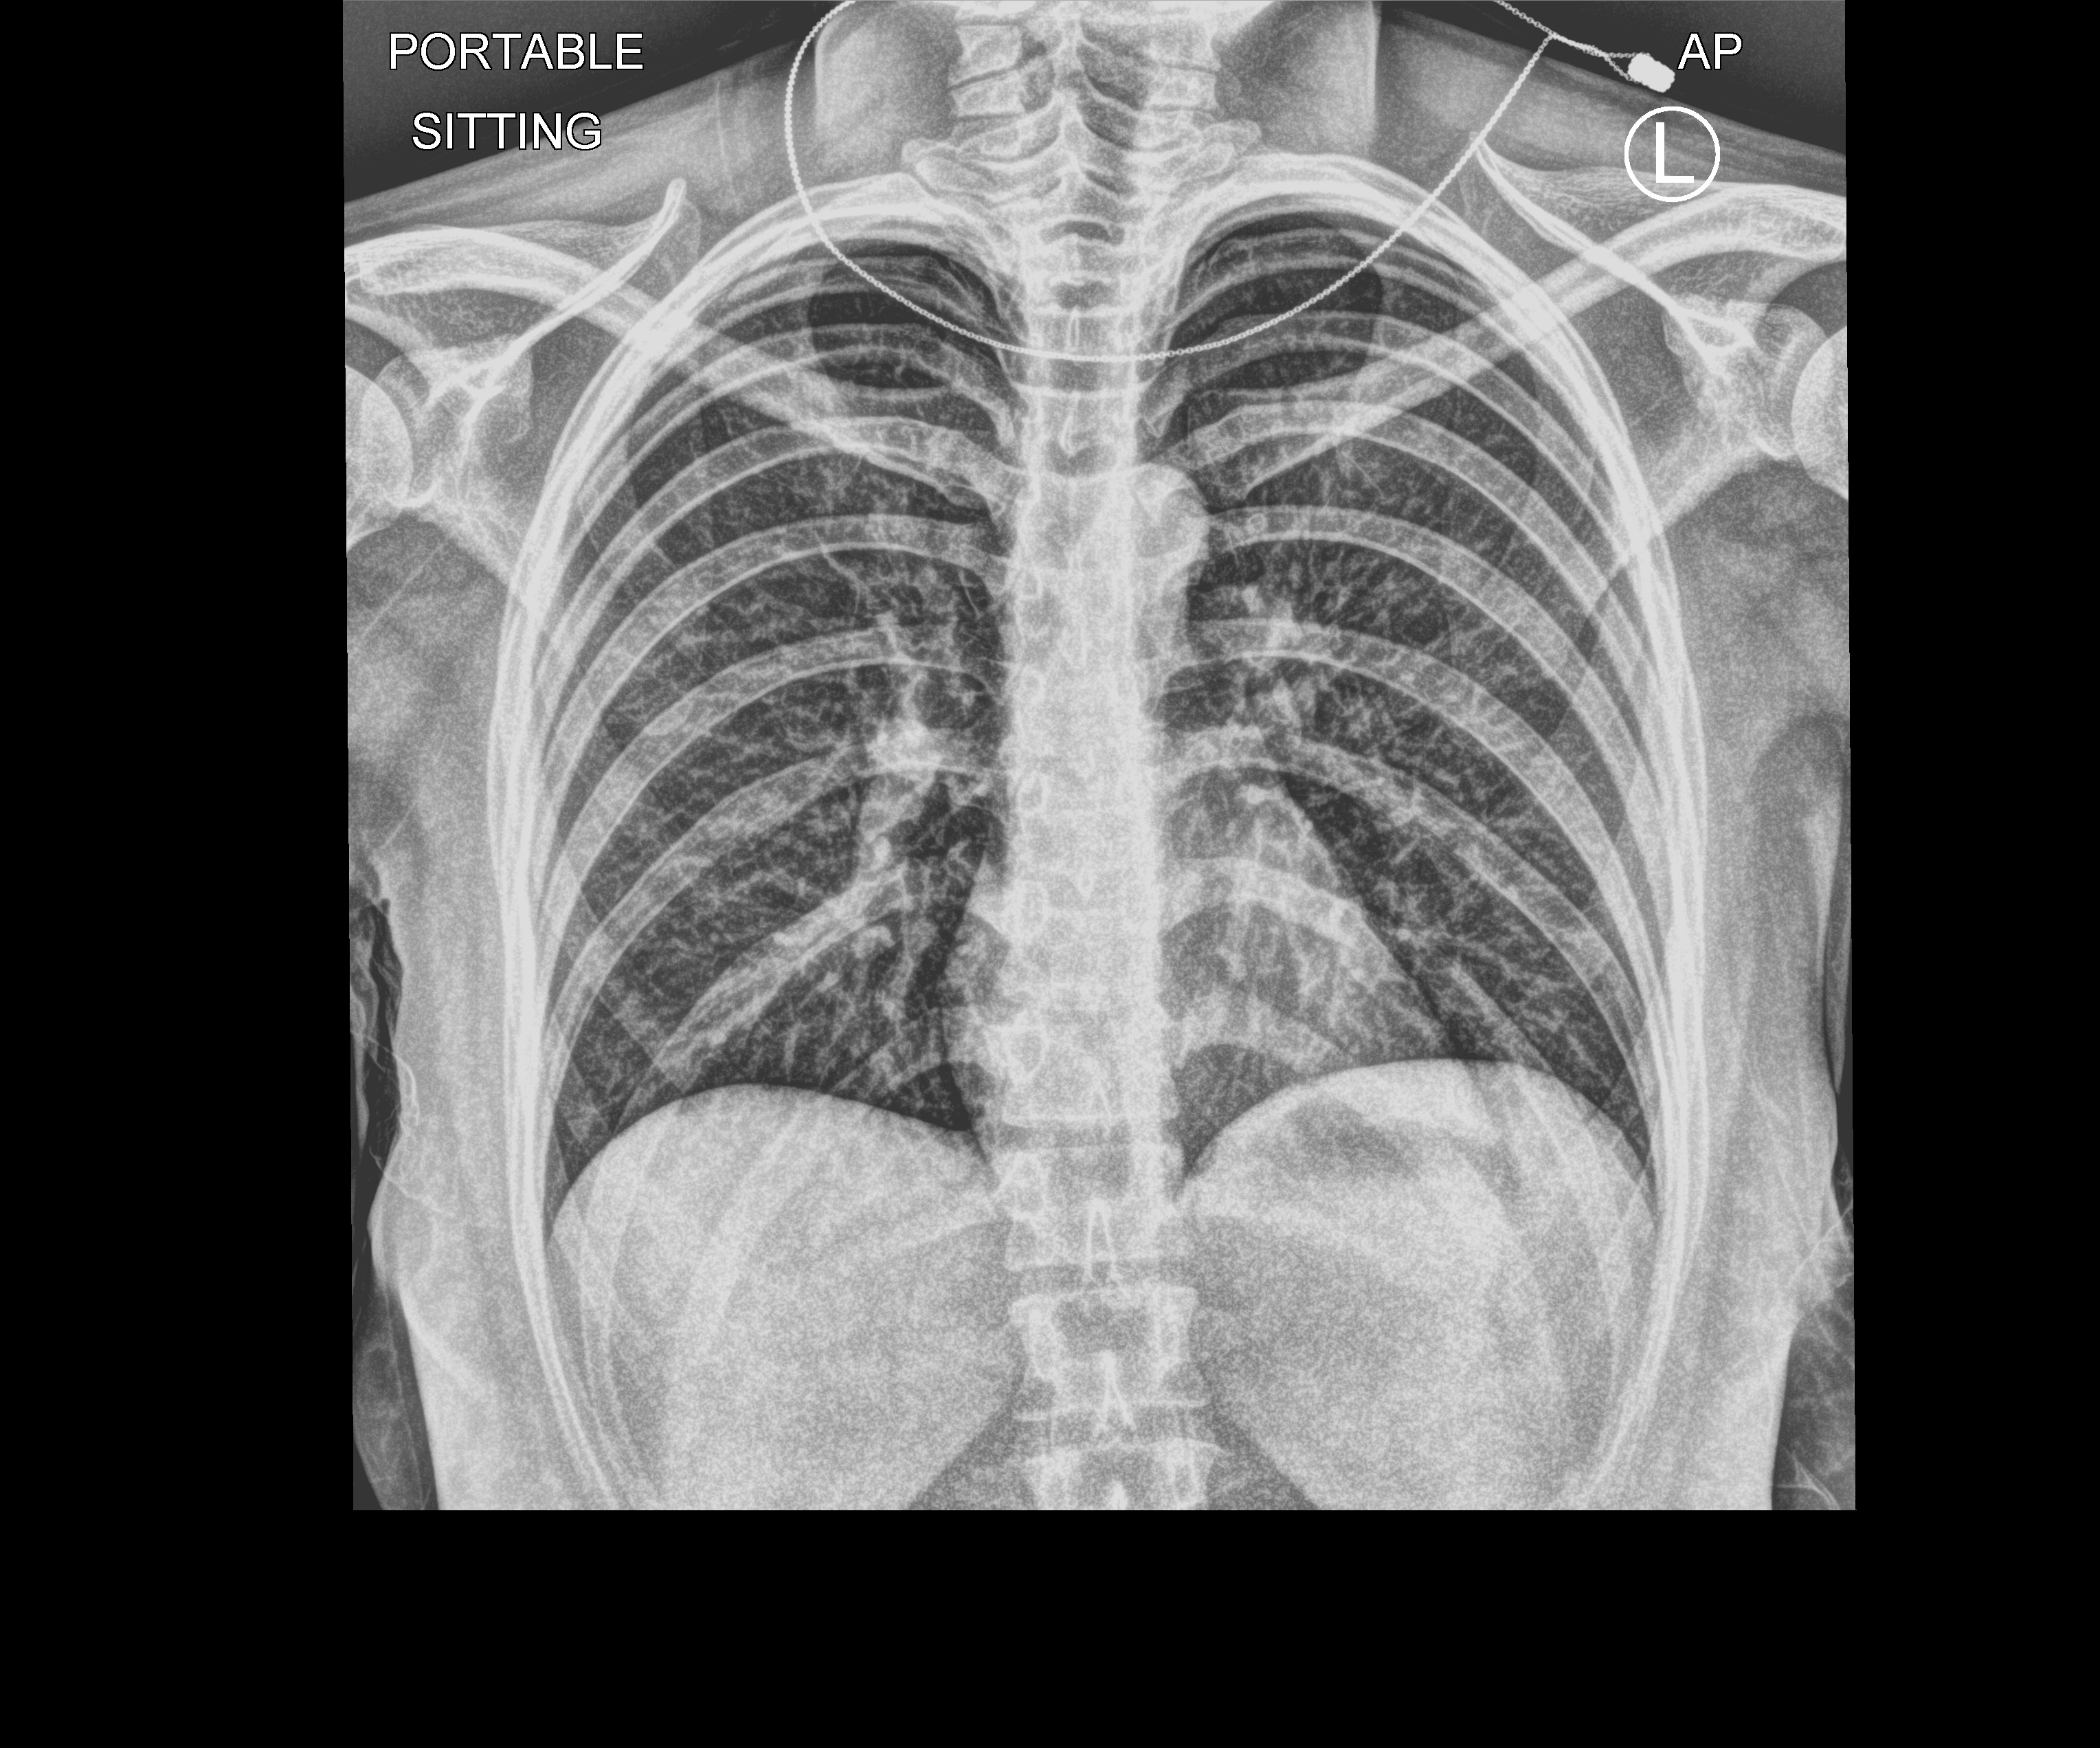
Chest X-ray (portable), anteroposterior (AP) projection. Female patient hospitalised with COVID-19, age 18–59 years.
From the hospital-stay record, not from the radiograph (when in the stay this image was taken is not recorded): mechanically ventilated during this hospital stay: no.